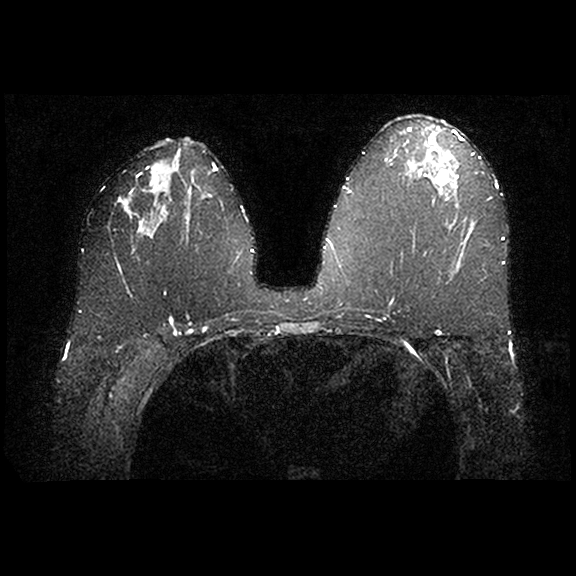
Breast MRI examination; 2 images, each one mid-volume slice chosen by position. Age decade 40s.
Image 1: fluid-sensitive (T2/STIR) axial slice, slice 43 of 84, 2 mm slice thickness.
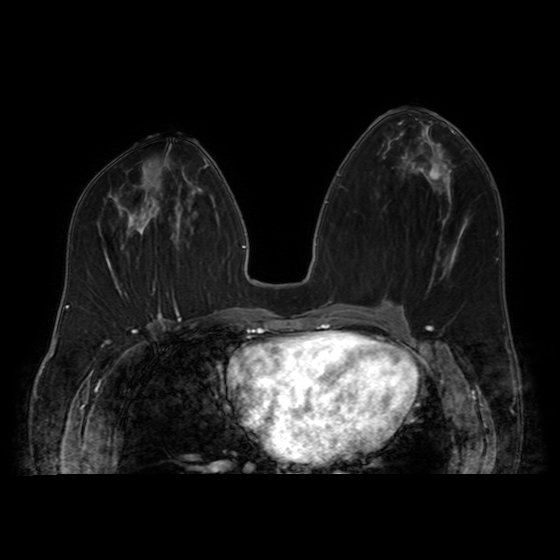
Image 2: axial dynamic contrast-enhanced T1-weighted image, slice 43 of 84, dynamic phase 5 of 8, 4 mm slice thickness.
MRI impression (as recorded): scattered bilateral cysts and fibroadenomas; BI-RADS 2.
Patient-level pathology facts (from the clinical record, not from the images): pathology diagnosis: benign fibroadenoma.